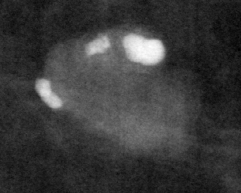
Region of interest cut from a scanned film mammogram (one marked finding), left breast, MLO view.
Finding: calcifications, morphology coarse; BI-RADS assessment category 2; subtlety rating 3 on a 1 (subtle) to 5 (obvious) scale; benign without callback (not worked up further).